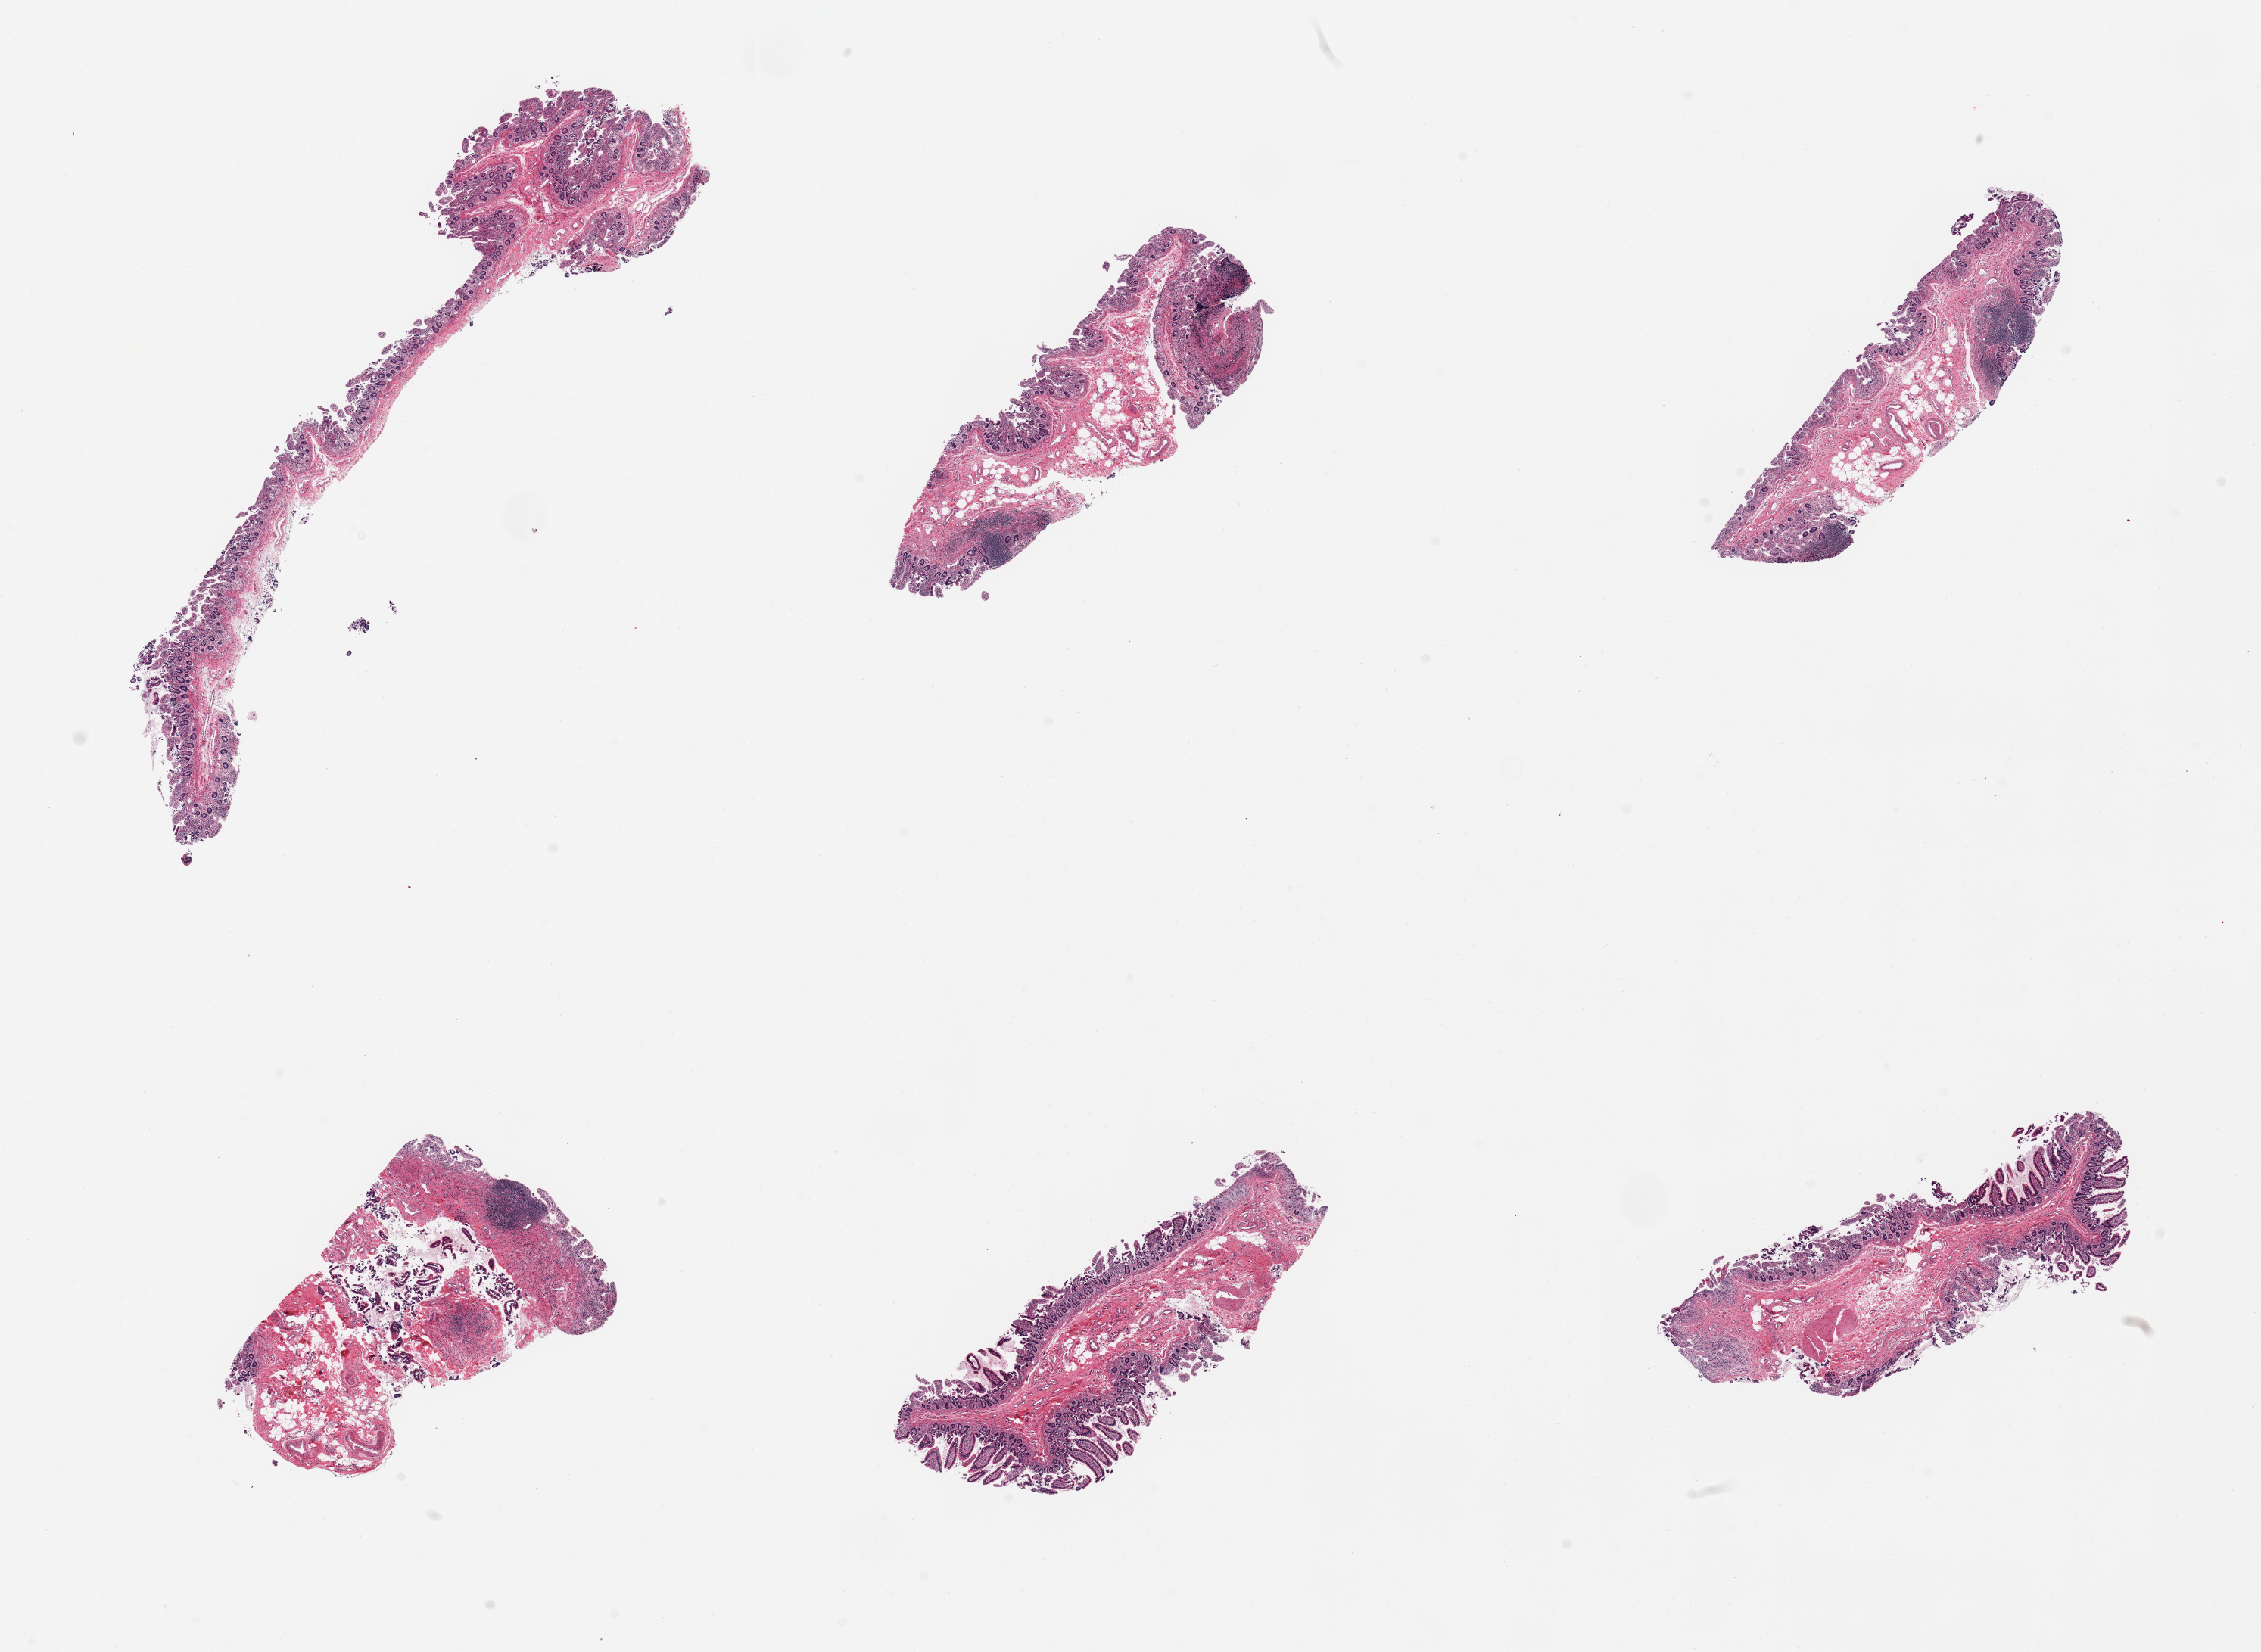
Whole-slide image, haematoxylin and eosin stain, low-resolution overview of the scanned area, about 23.6 x 17.3 mm (acquisition: 20x scan). PAXgene-fixed paraffin-embedded (PFPE) section. Target tissue: ileum. Donor tissue sample. Male donor.
* review note (as recorded): 6 pieces, lymphoid aggregates are ~10-20%